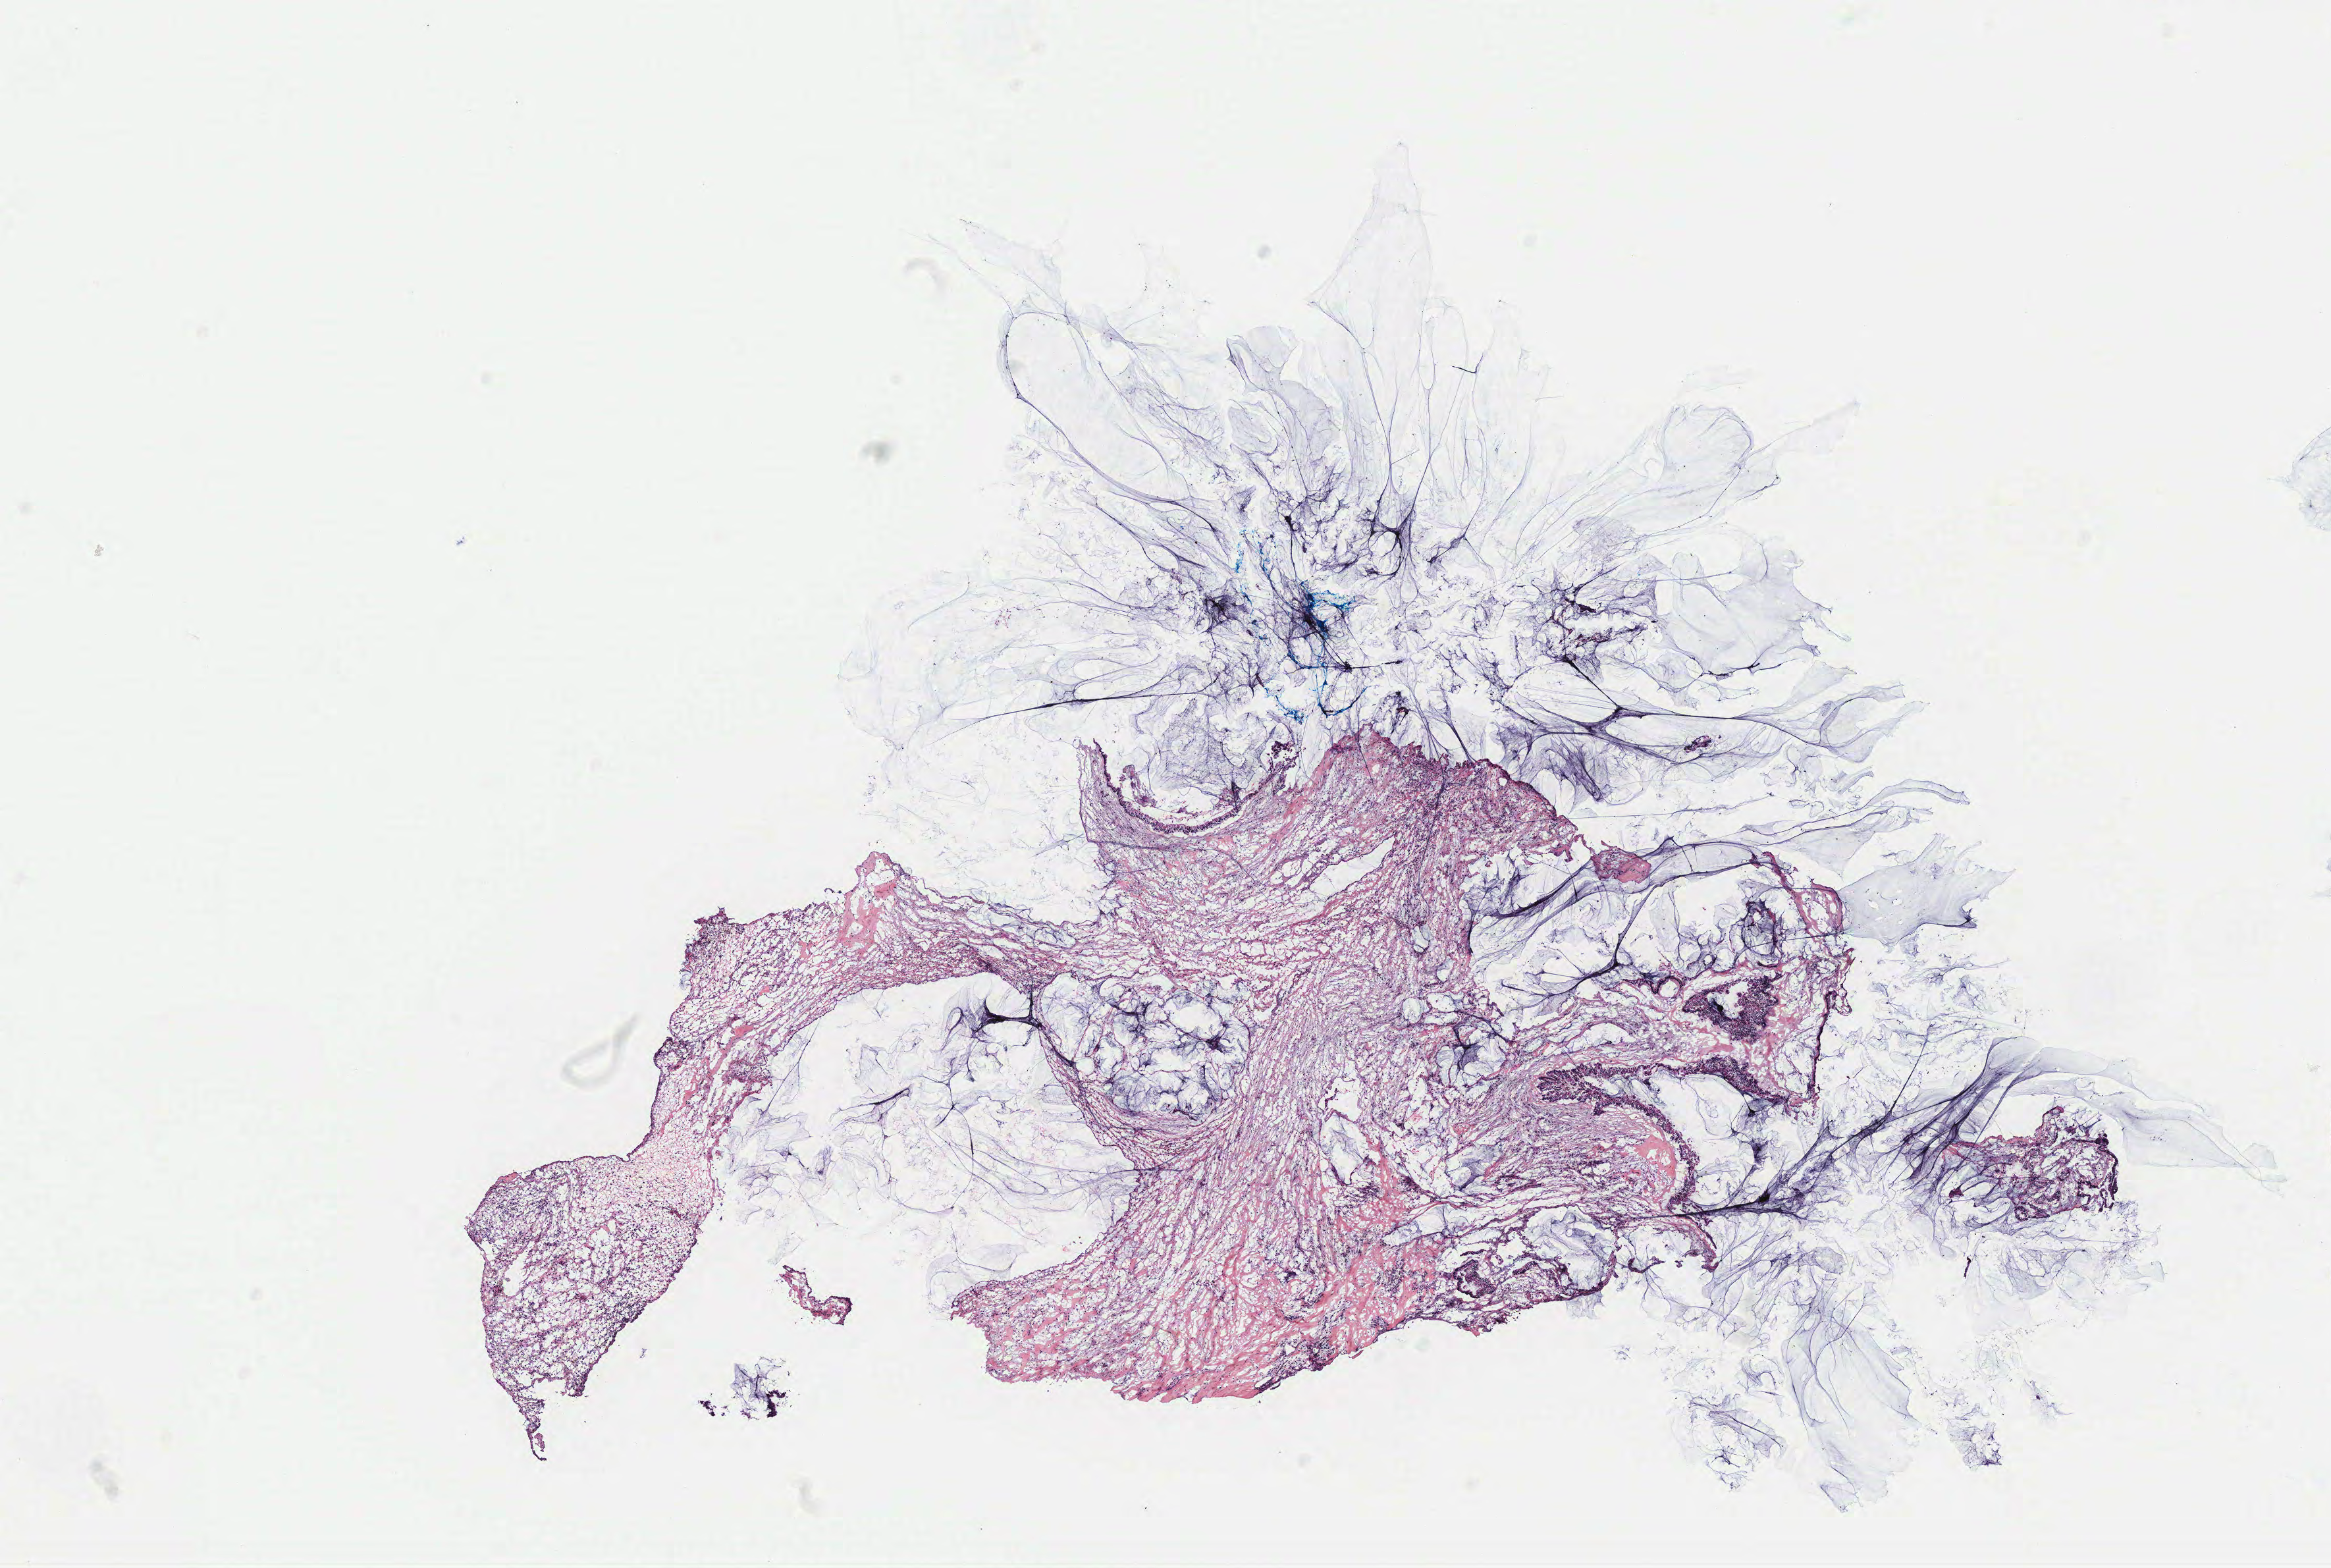
Digitized H&E tissue section (whole slide) — low-resolution overview of the scanned area, about 14.2 x 9.5 mm; colon, tissue type not recorded.
Patient diagnosis (cohort enrolment): colon cancer (colon).